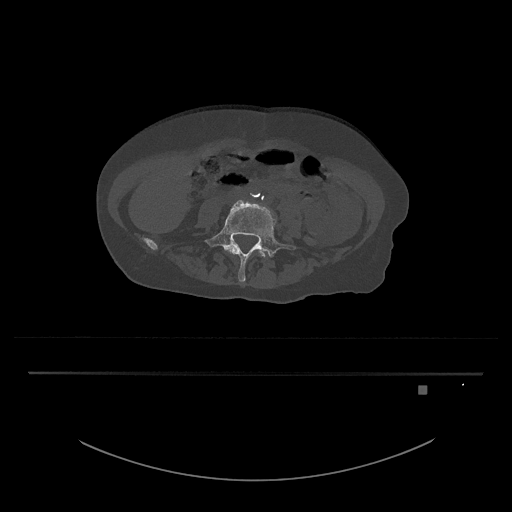
CT including the spine, one axial slice; slice 315 of 797 in the series (ordered by position); 120 kVp; bone window (W 1800 / L 400 HU); 512 × 512 image matrix, field of view 500 × 500 mm. Female patient, age 57 years. From the clinical record (not read from this slice): primary cancer: cervical.
Outlined on this slice (semi-automatic segmentation, software-assisted and operator-edited):
- L4 vertebra: bounding box <224,242,270,258> (left, top, right, bottom; pixels)